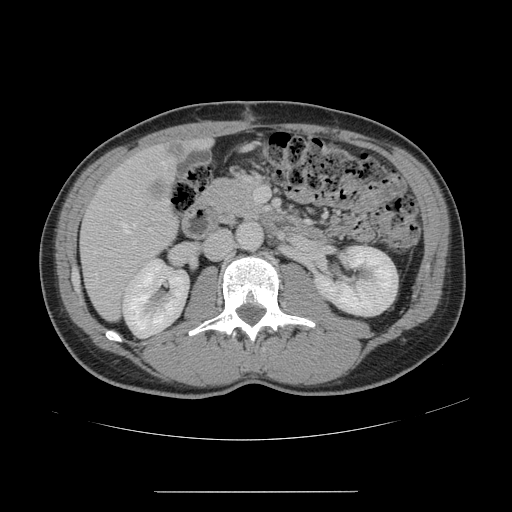
Contrast-enhanced abdominal CT, one axial slice; position 61 of 178 along the scan axis; 120 kVp; intravenous contrast given; soft-tissue window (W 400 / L 40 HU); 512 × 512 image matrix. Male patient, age 53 years. From the clinical record (not read from this slice): diagnosis: colorectal cancer liver metastases, imaged before liver resection; multiple liver metastases: yes; largest metastasis: 2.4 cm.
Annotated regions visible in this slice (expert manual segmentation):
- hepatic veins: box from (x=96, y=161) to (x=165, y=275) px
- liver: (x=81, y=140)–(x=202, y=319)
- portal vein (with intrahepatic branches): (x=254, y=187)–(x=267, y=202)
- liver metastasis: (x=167, y=143)–(x=188, y=158)
- liver metastasis: (x=148, y=180)–(x=169, y=201)